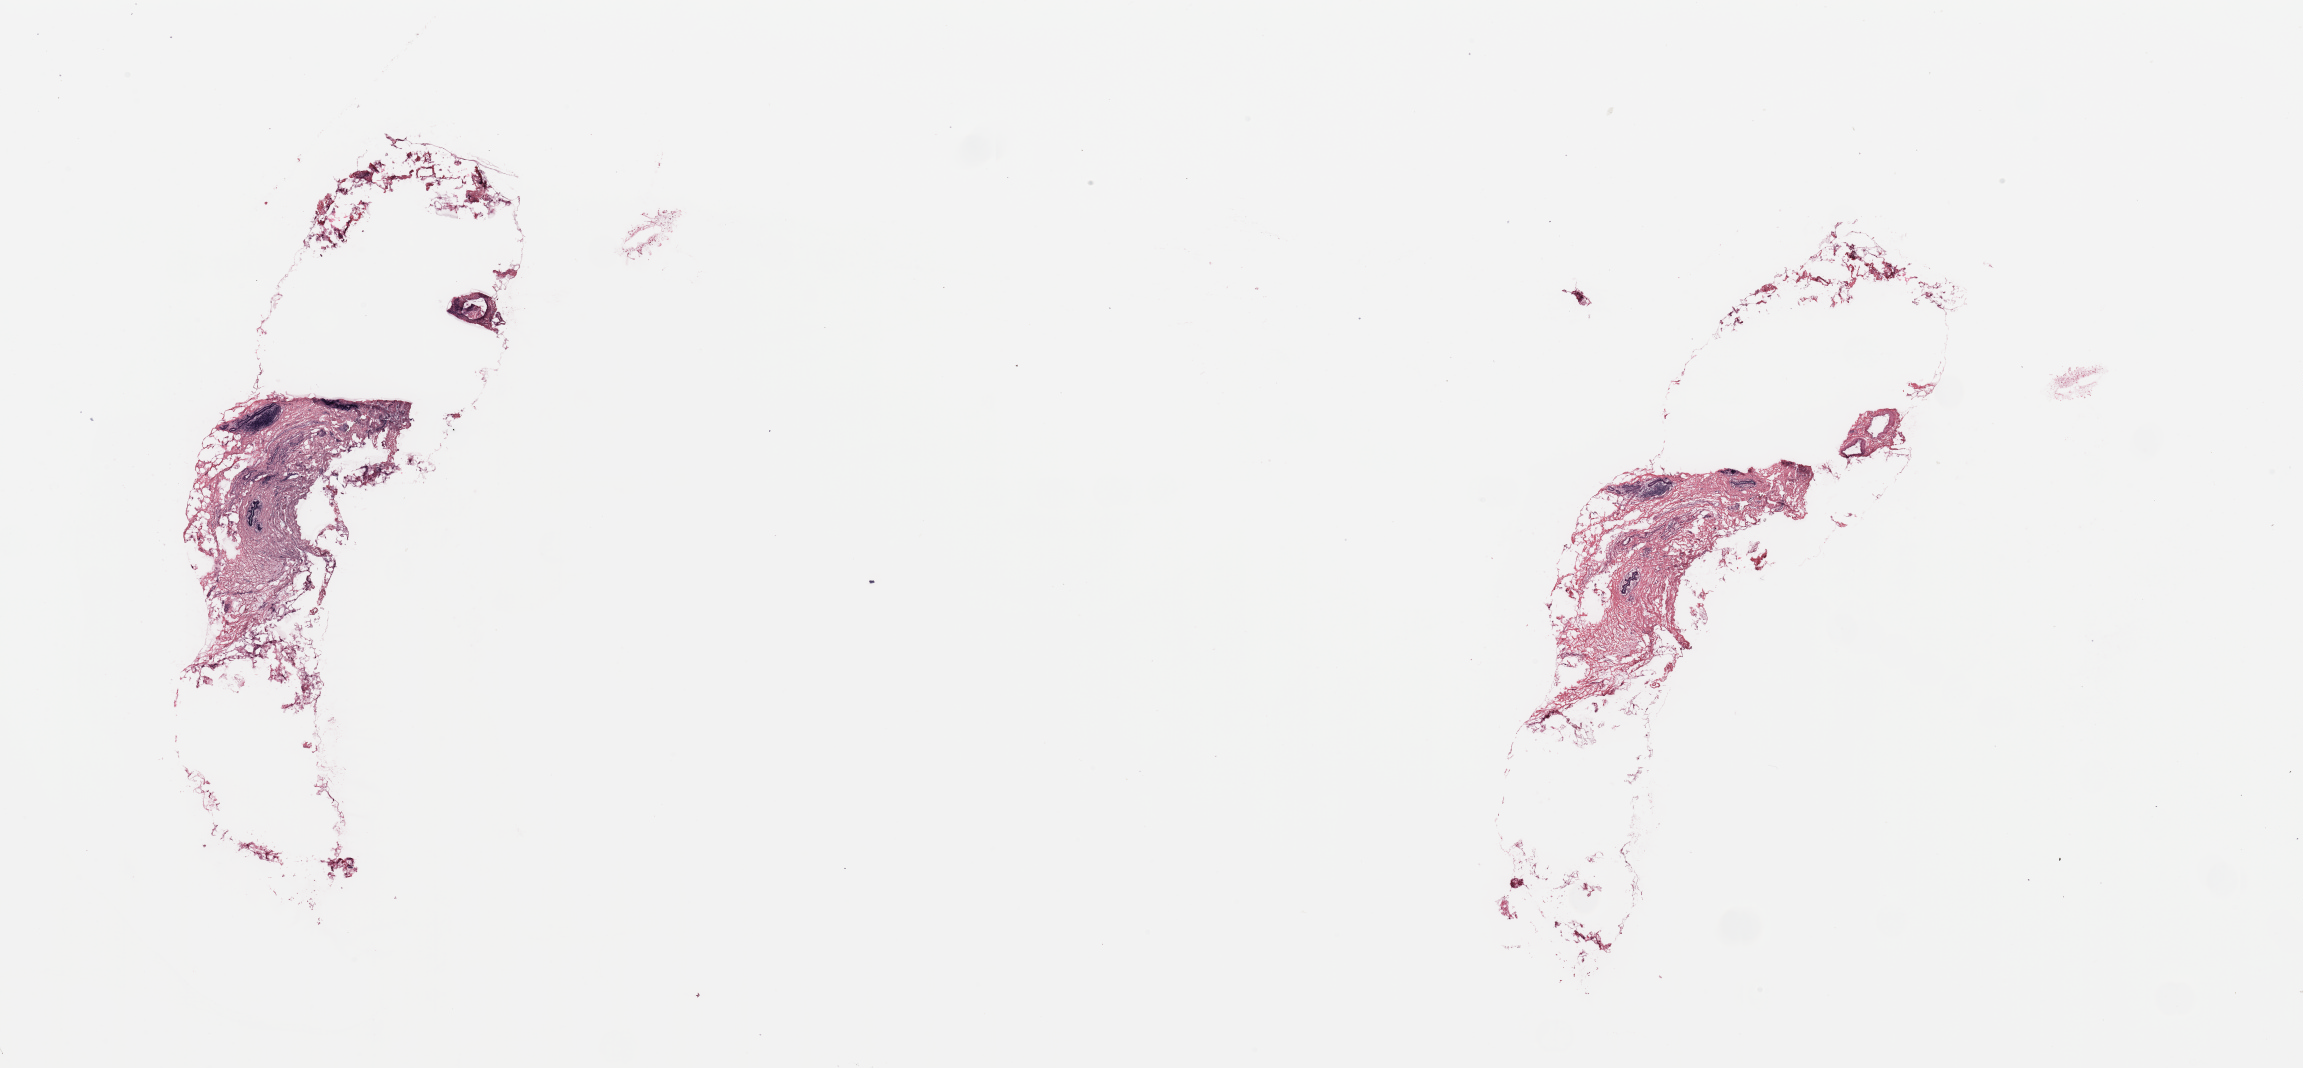
Digitized Hematoxylin and eosin (H&E) stained tissue section (whole slide), shown as a low-resolution overview of the whole scanned area (about 36.4 x 16.9 mm, from a 20x scan), breast, tissue type not recorded.
Patient diagnosis (cohort enrolment): breast cancer (breast).